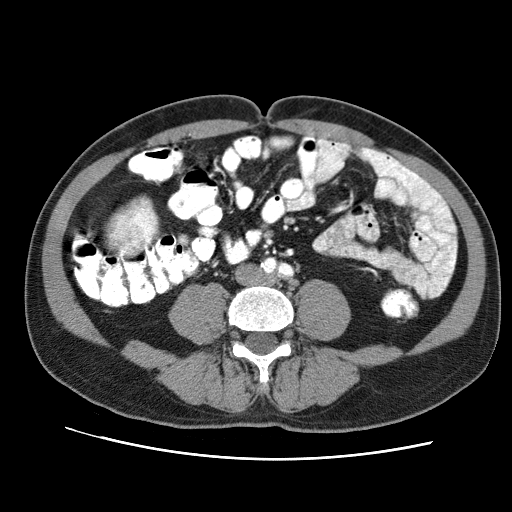
Contrast-enhanced abdominal CT (liver protocol), one axial slice. Position 5 of 71 along the scan axis. Reconstruction kernel STANDARD. 120 kVp. Soft-tissue window (W 400 / L 40 HU). 2.5 mm slice thickness. 512 × 512 image matrix, field of view 360 × 360 mm. From the clinical record (not read from this slice): diagnosis: hepatocellular carcinoma (patient treated with transarterial chemoembolisation; whether this scan precedes or follows treatment is not stated here); TNM stage (as recorded): Stage-II; Child-Pugh class: A; tumour differentiation: well differentiated; tumour nodularity: multinodular.
Structures marked on this image (semi-automatically segmented with operator editing):
- mass: box from (x=109, y=201) to (x=157, y=252) px